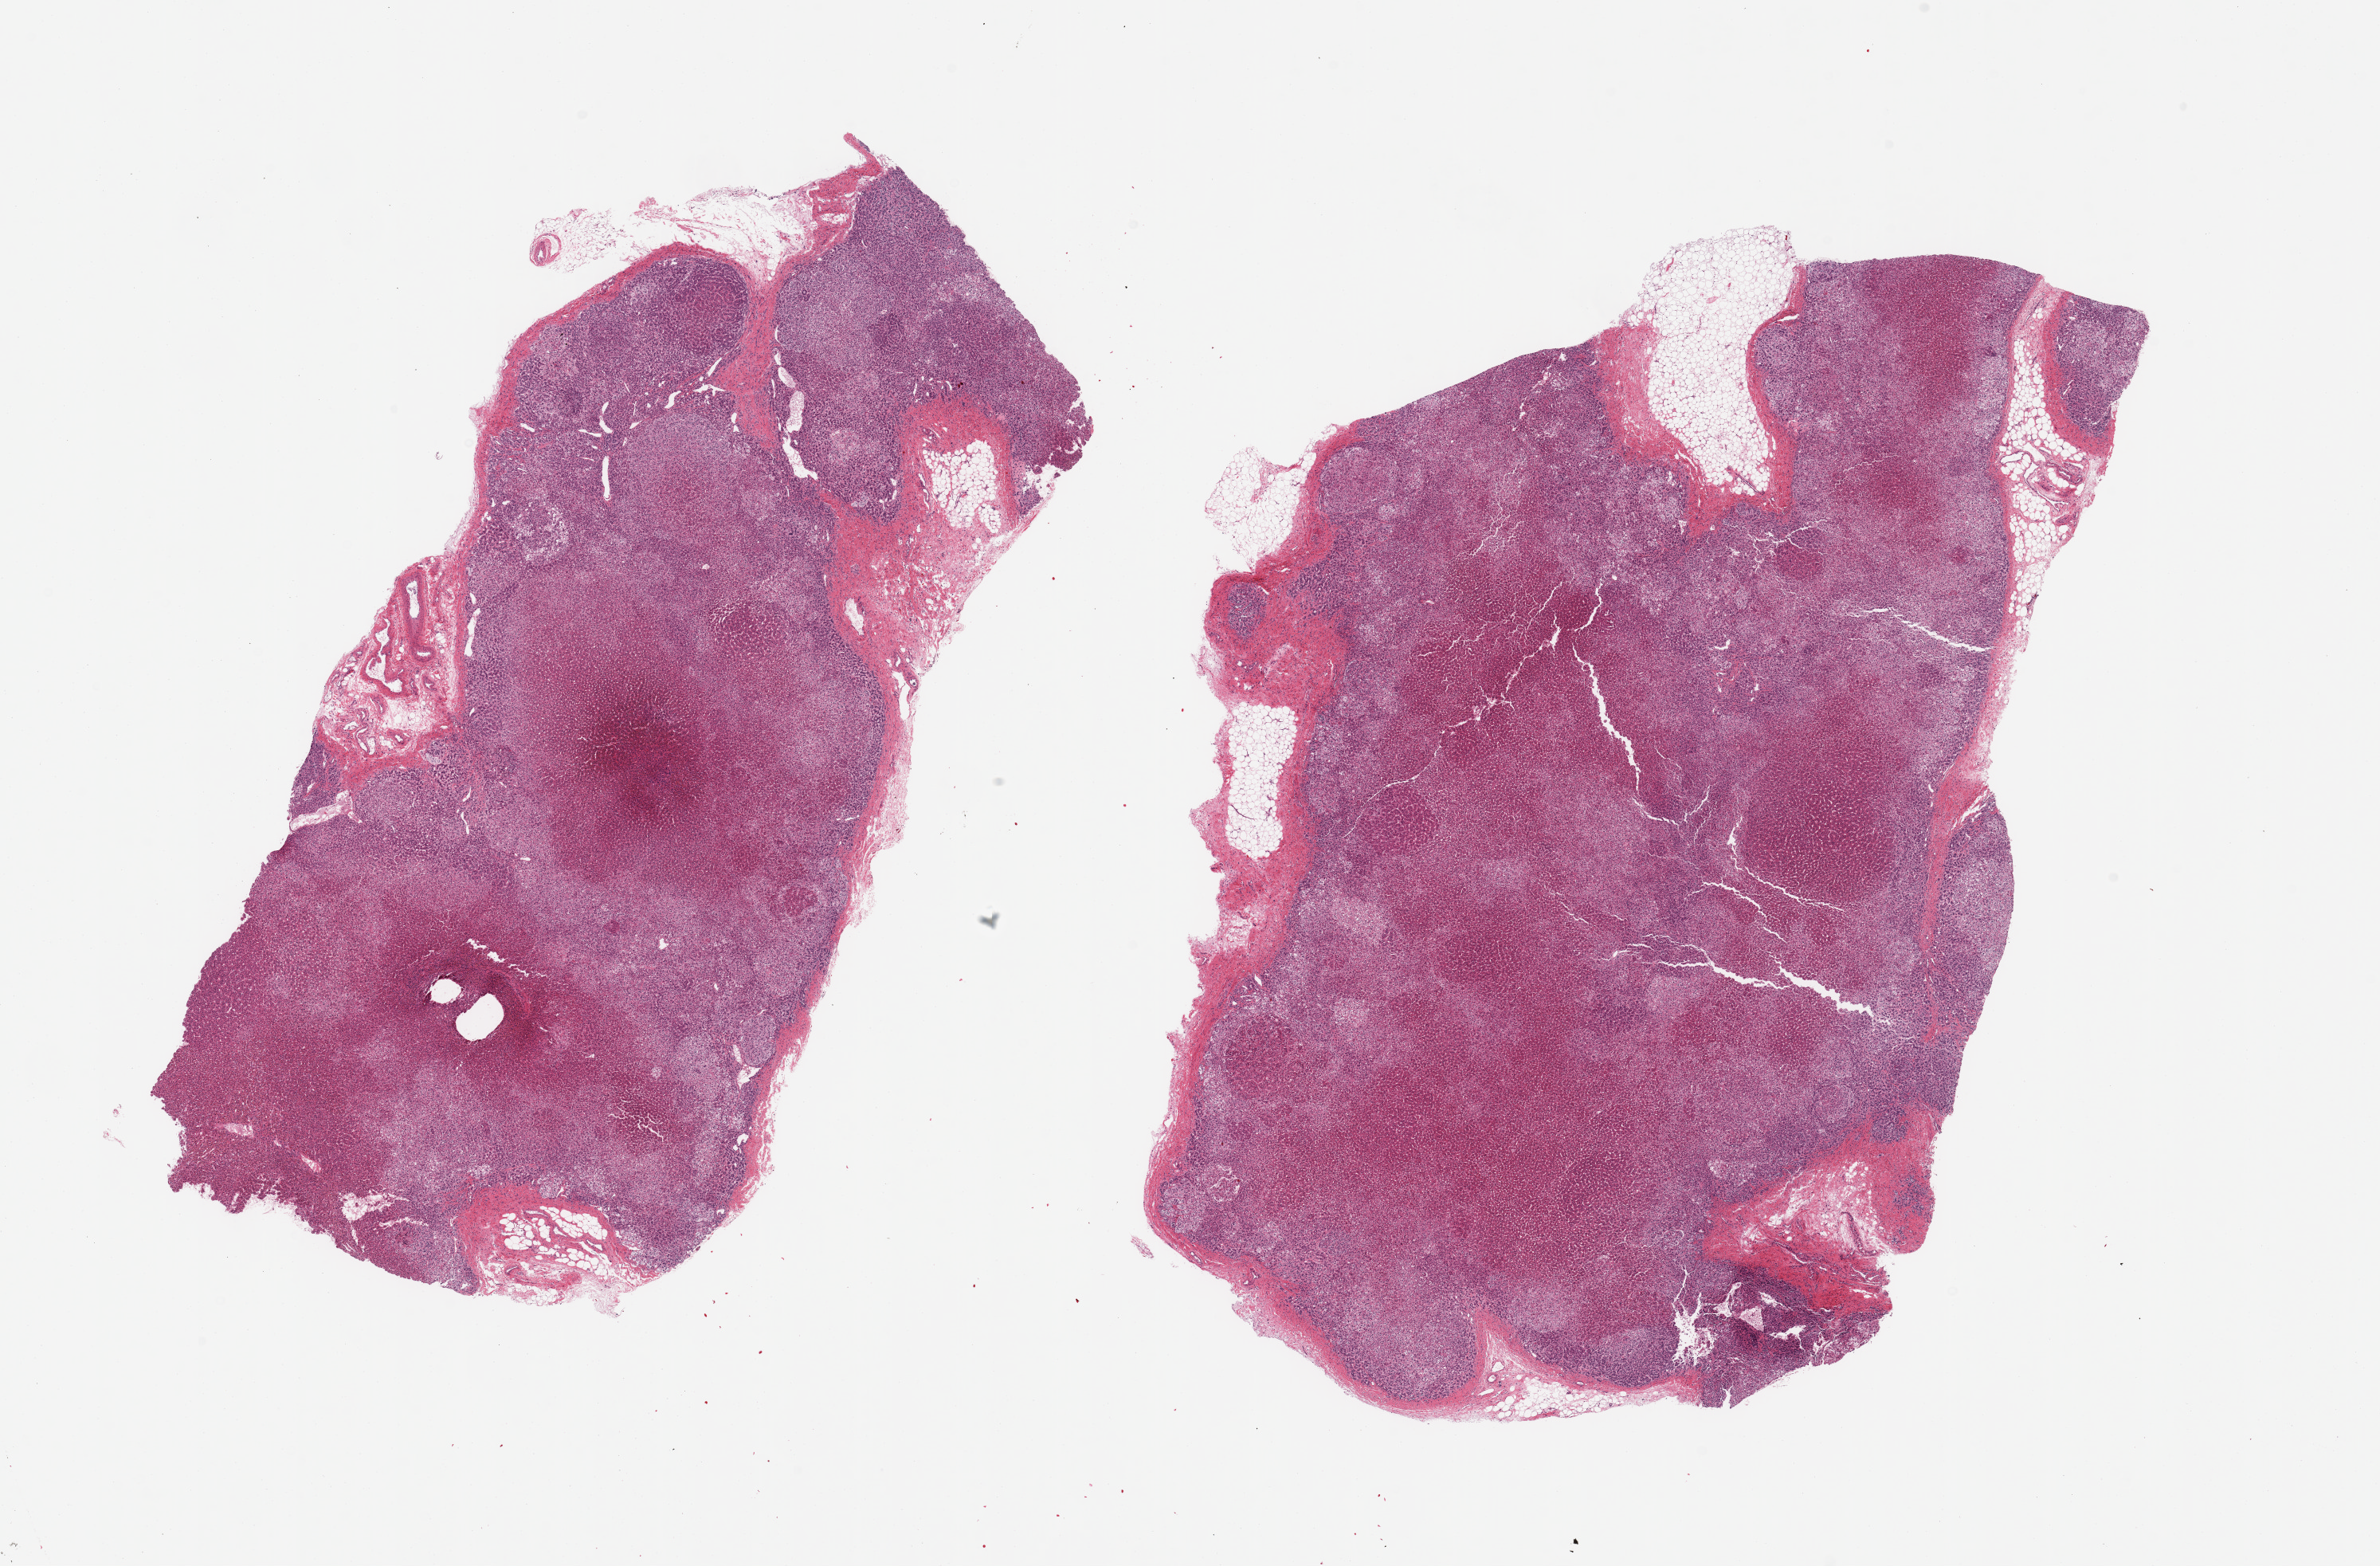
Whole-slide image, hematoxylin and eosin (H&E) stain — shown as a low-resolution overview of the whole scanned area (about 23.6 x 15.5 mm, from a 20x scan); PAXgene-fixed, paraffin-embedded tissue; section of adrenal gland (target tissue); tissue donor sample. Female donor.
Reviewer comment on this tissue sample: 2 pieces, cortex, nubbins of adherent fat up to ~1-2mm.